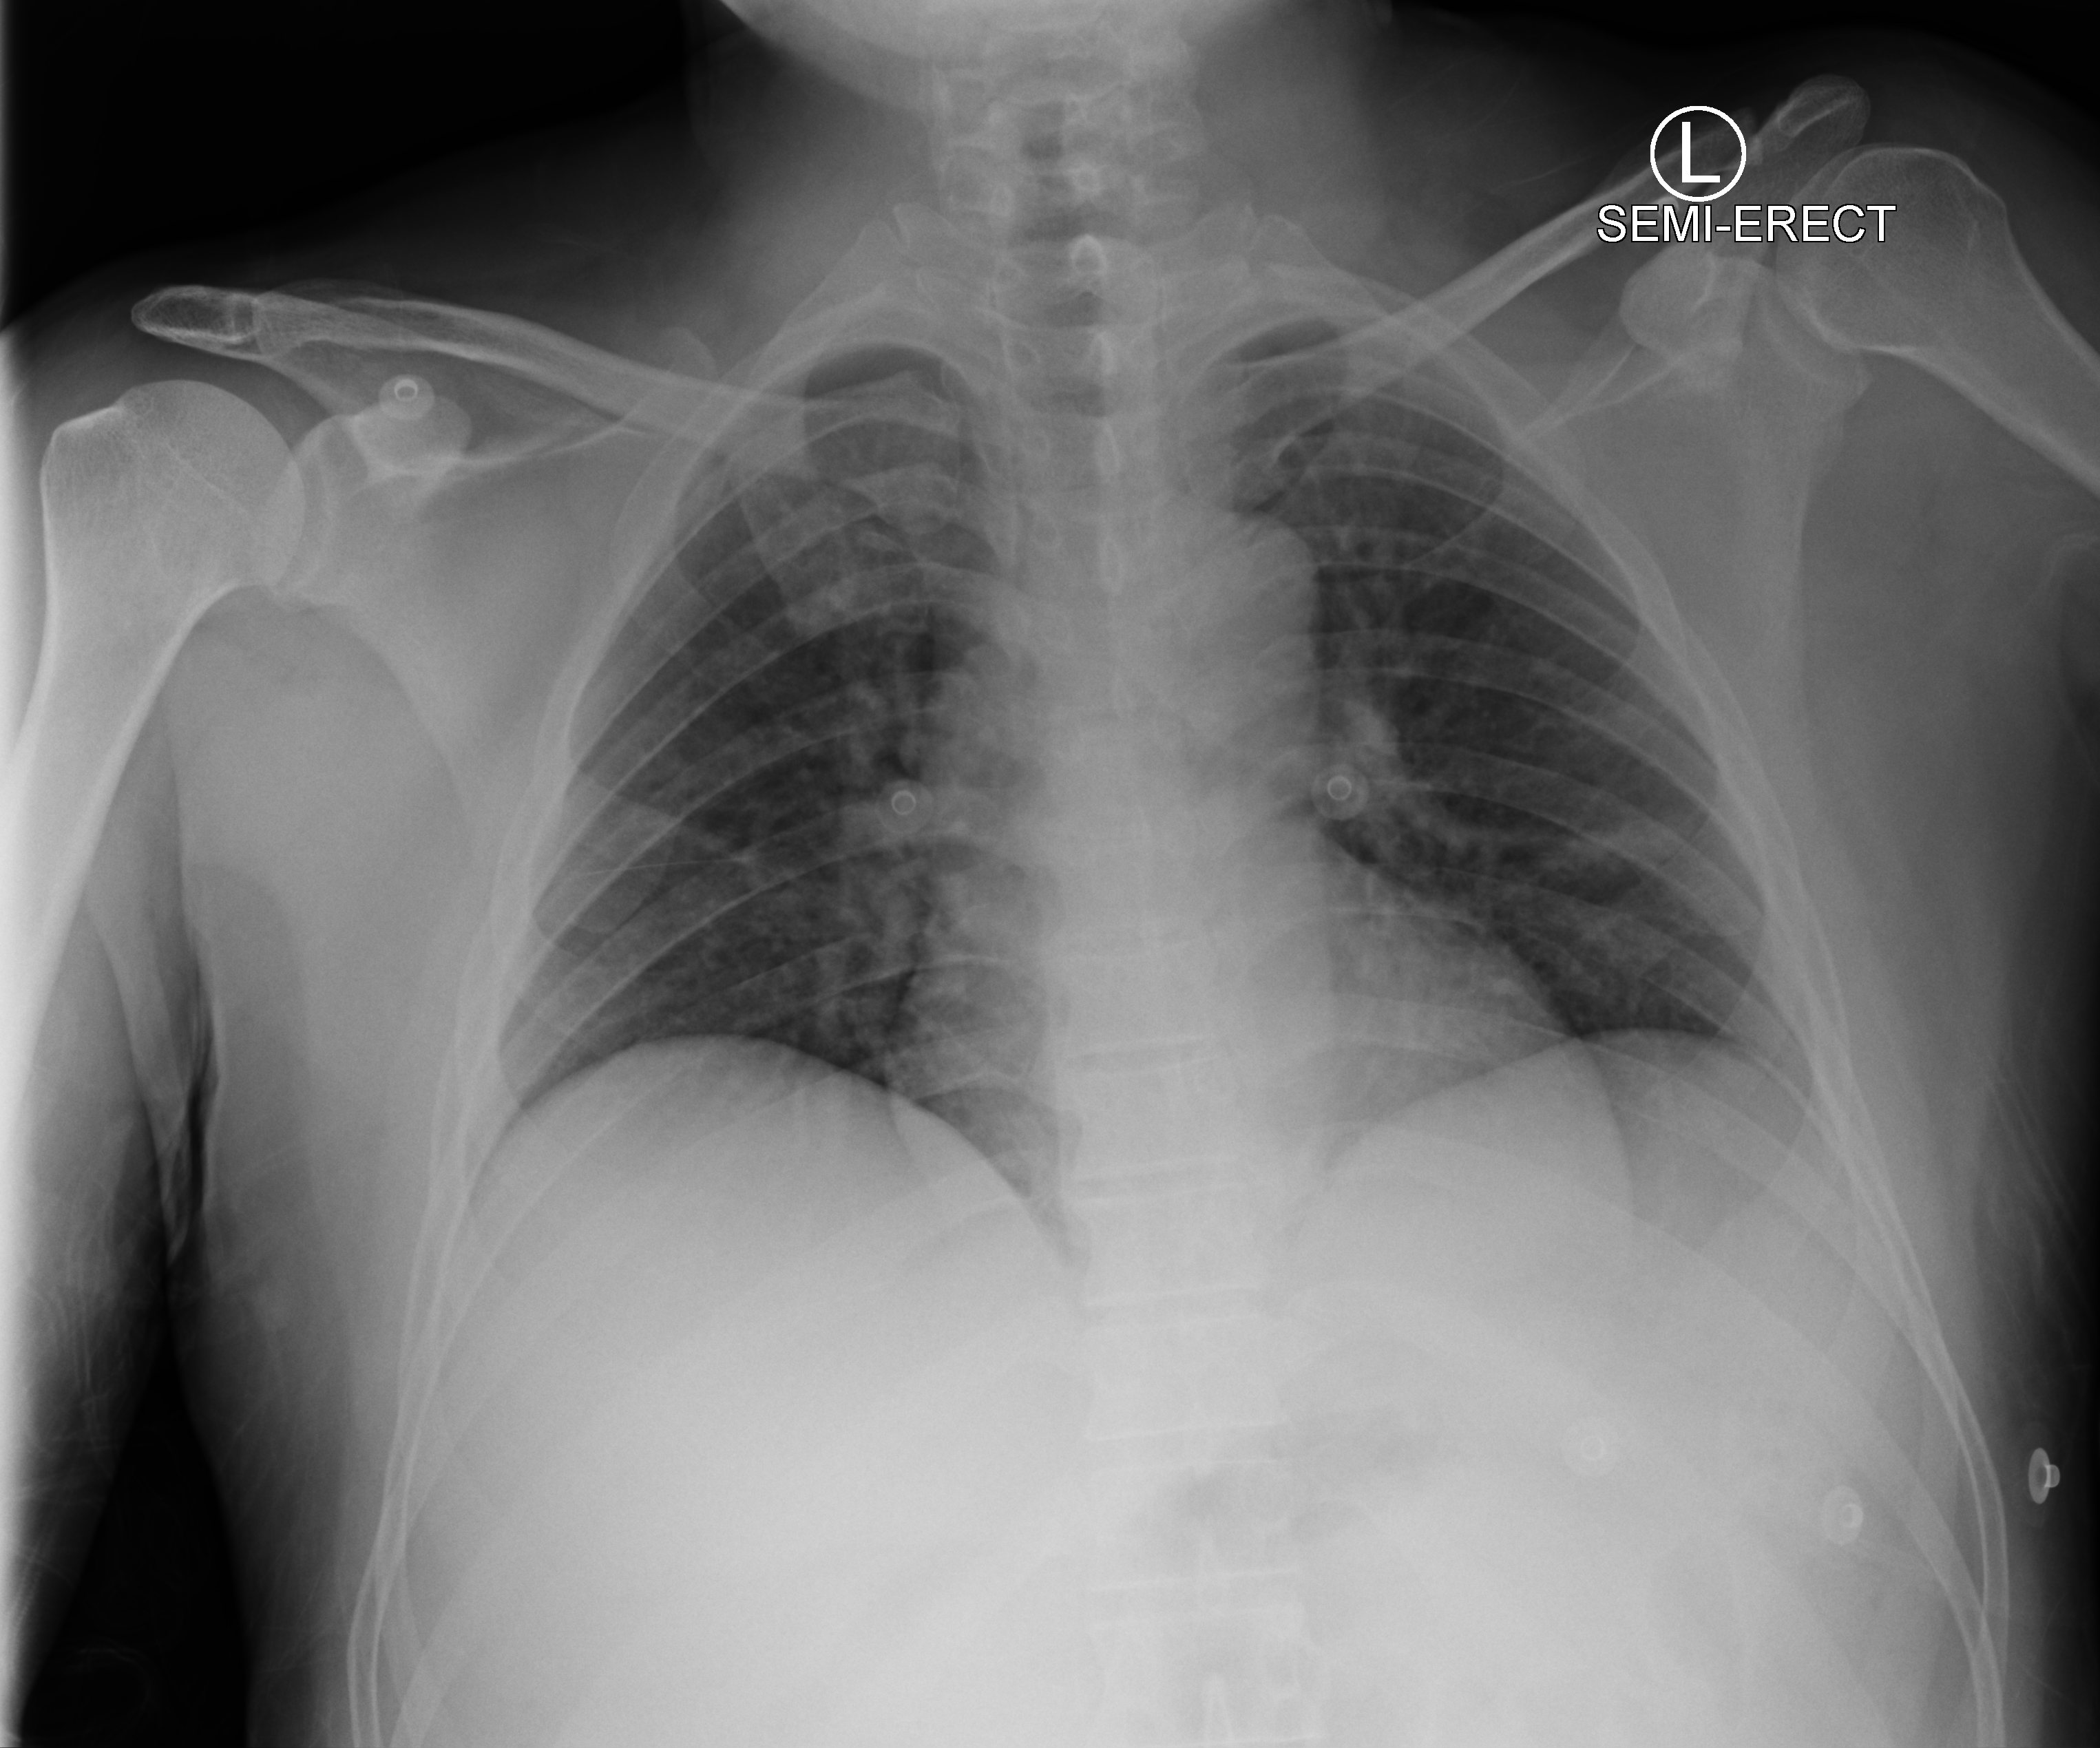
Bedside chest radiograph (computed radiography), anteroposterior (AP) projection. Patient hospitalised with COVID-19; male, aged 18–59 years.
Hospital-stay facts (about this admission, not read from this image; timing relative to this image not recorded):
- admitted to intensive care during this hospital stay: no